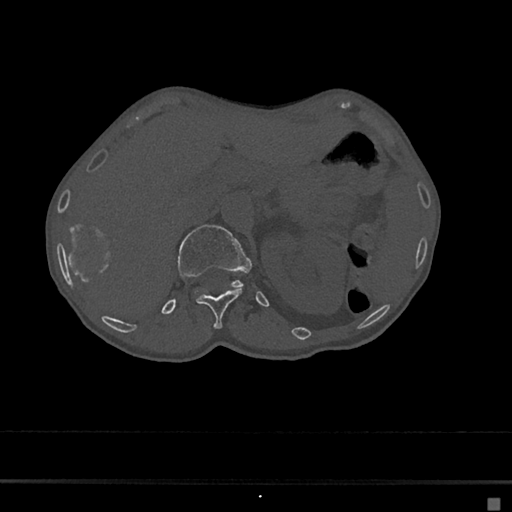
CT including the spine, one axial slice. Position 102 of 797 along the scan axis. Reconstruction kernel Br40s/3. Bone window (W 1800 / L 400 HU). 0.5 mm slice thickness. 512 × 512 image matrix. Patient: female, 68 years. Case-level facts recorded for this patient, not image findings: primary cancer: renal.
Structures marked on this image (semi-automatically segmented with operator editing):
- L1 vertebra: box from (x=176, y=224) to (x=252, y=288) px
- T12 vertebra: (x=196, y=290)–(x=241, y=329)